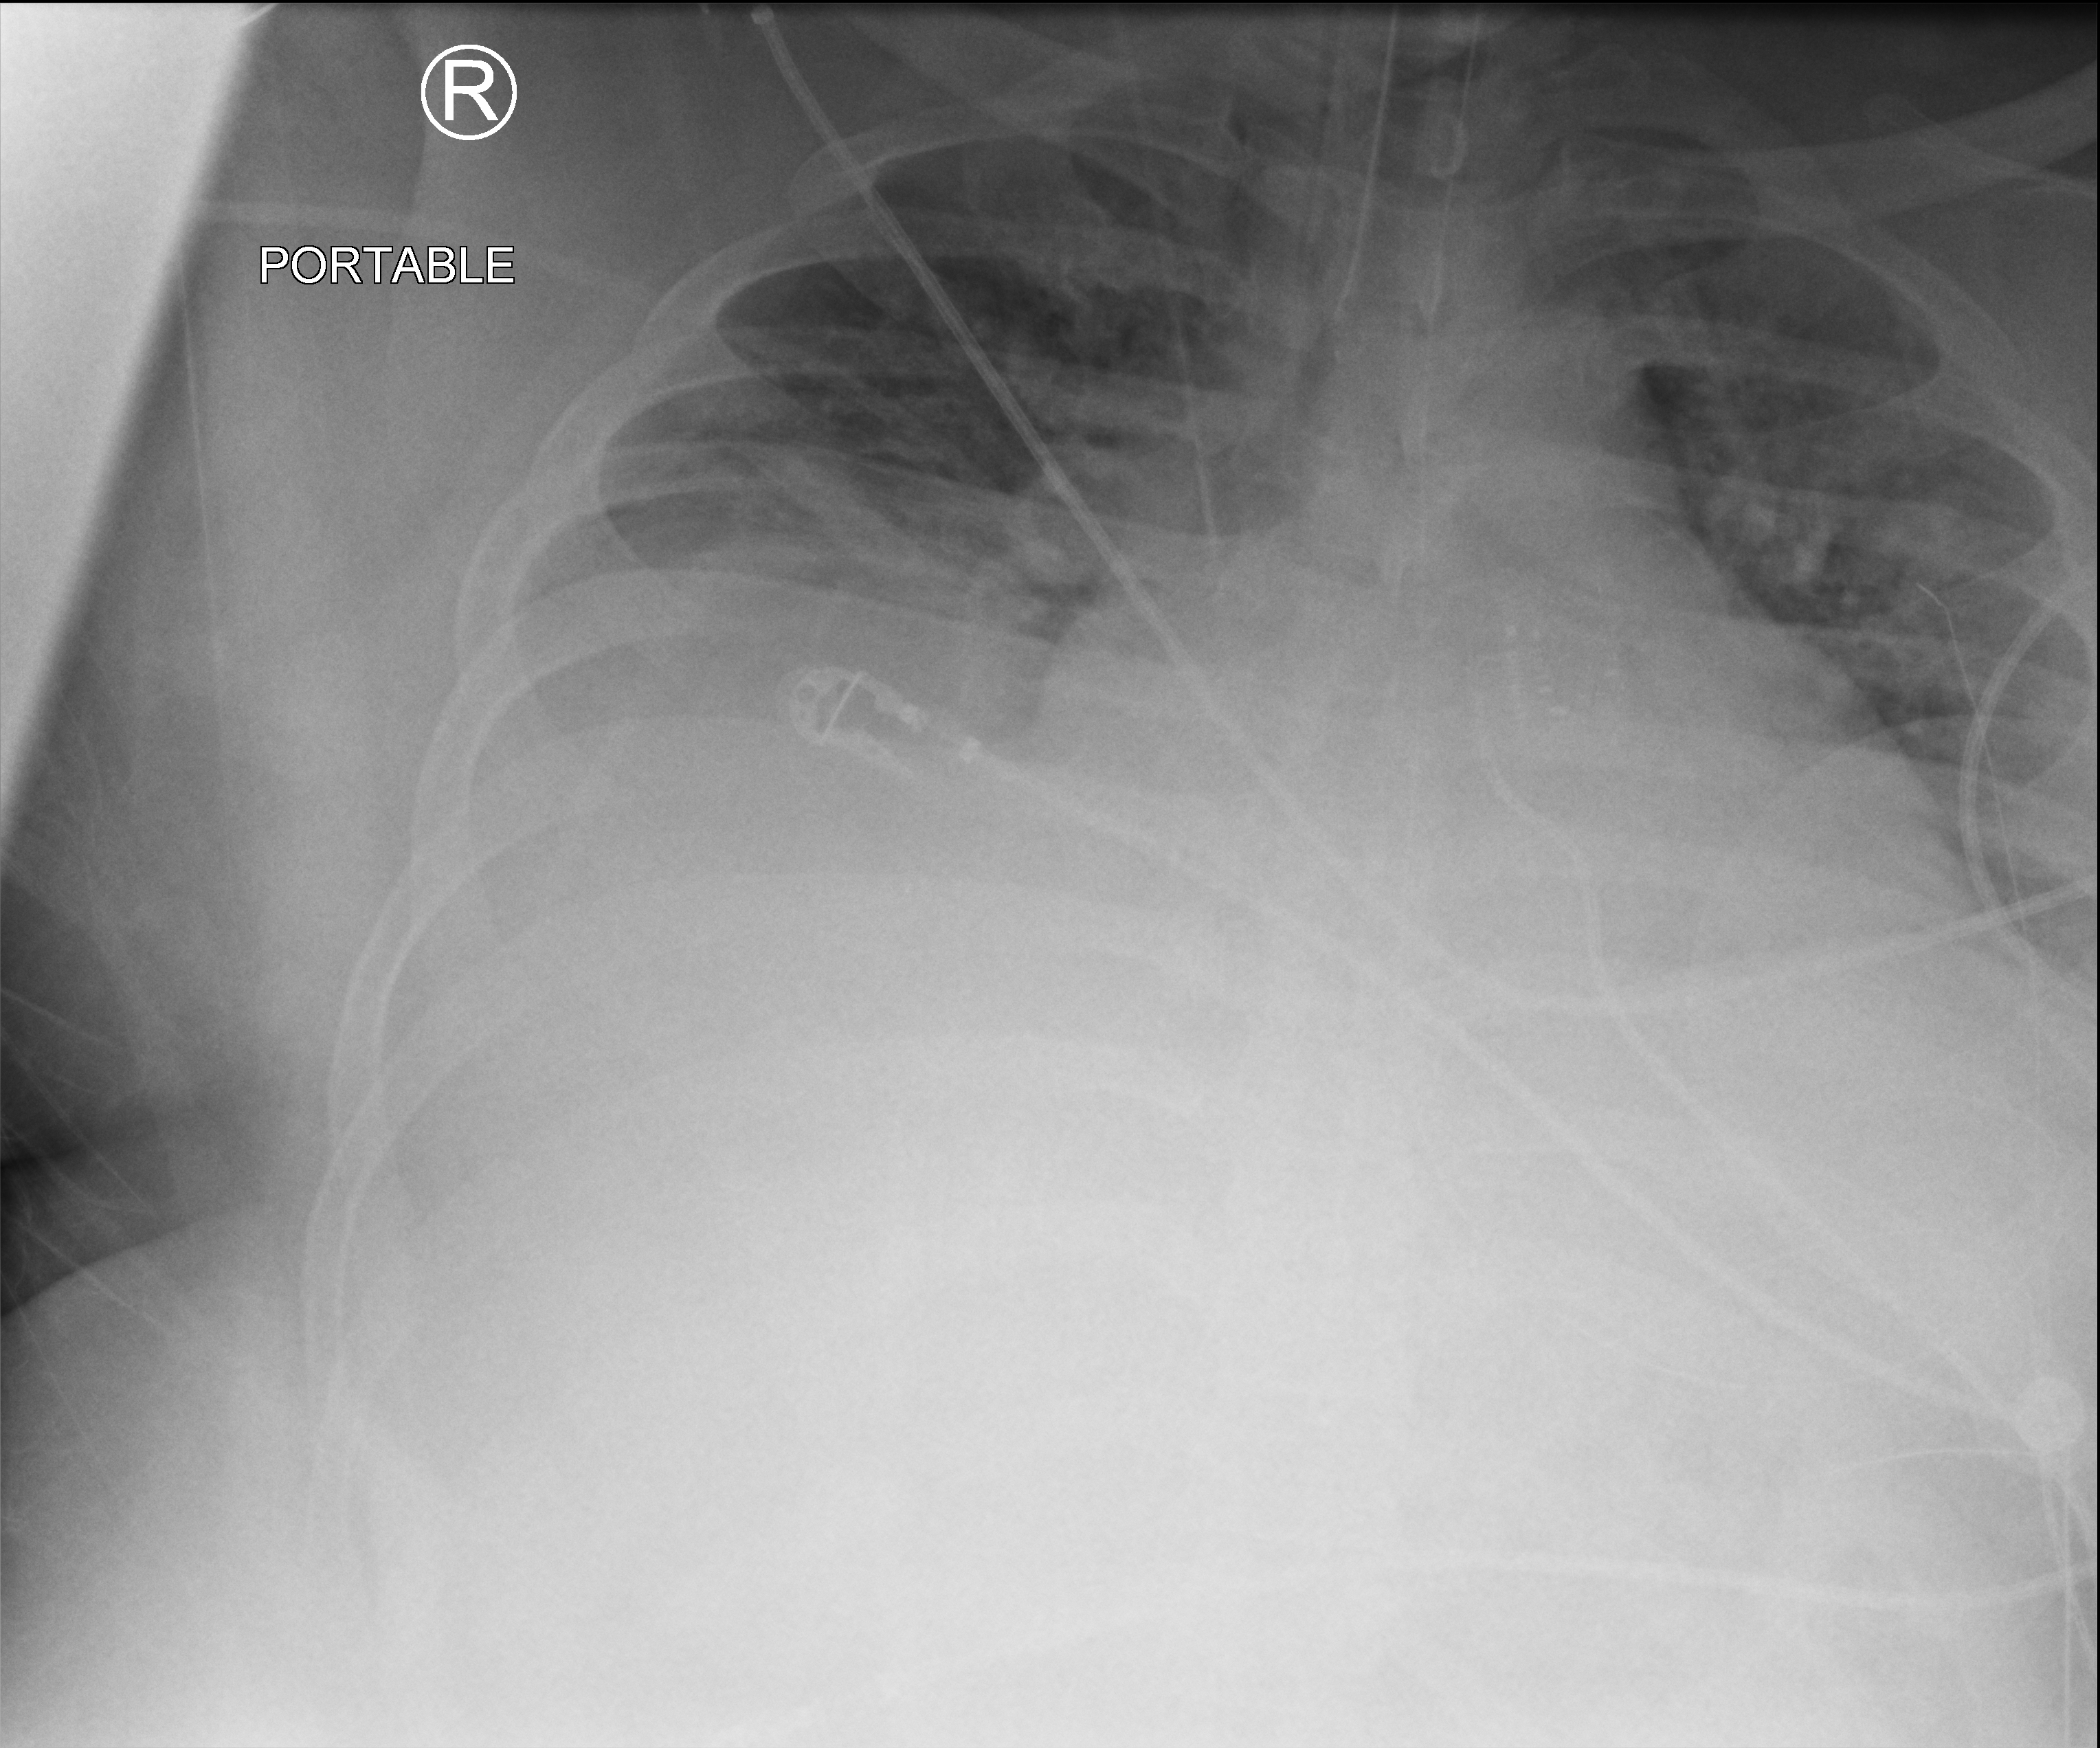
Chest X-ray (portable); anteroposterior (AP) projection. Male patient hospitalised with COVID-19, age 18–59 years.
Admission-level facts for this patient (not findings on this image; timing relative to this image not recorded):
- hypertension (admission record): no